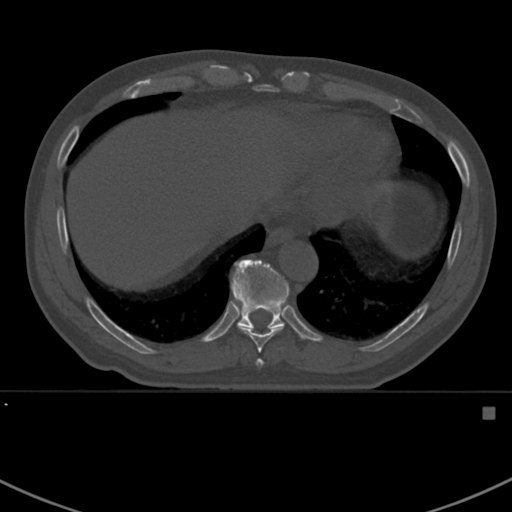
CT including the spine, one axial slice. Position 376 of 412 along the scan axis. Reconstruction kernel Br40s. 120 kVp. Bone window (W 1800 / L 400 HU). 1.5 mm slice thickness. 512 × 512 image matrix, field of view 358 × 358 mm. Patient: male, 59 years. Case-level facts recorded for this patient, not image findings: primary cancer: prostate.
Structures marked on this image (semi-automatically segmented with operator editing):
- T10 vertebra: box from (x=231, y=259) to (x=289, y=329) px
- T8 vertebra: (x=256, y=359)–(x=264, y=367)
- T9 vertebra: (x=239, y=327)–(x=283, y=353)